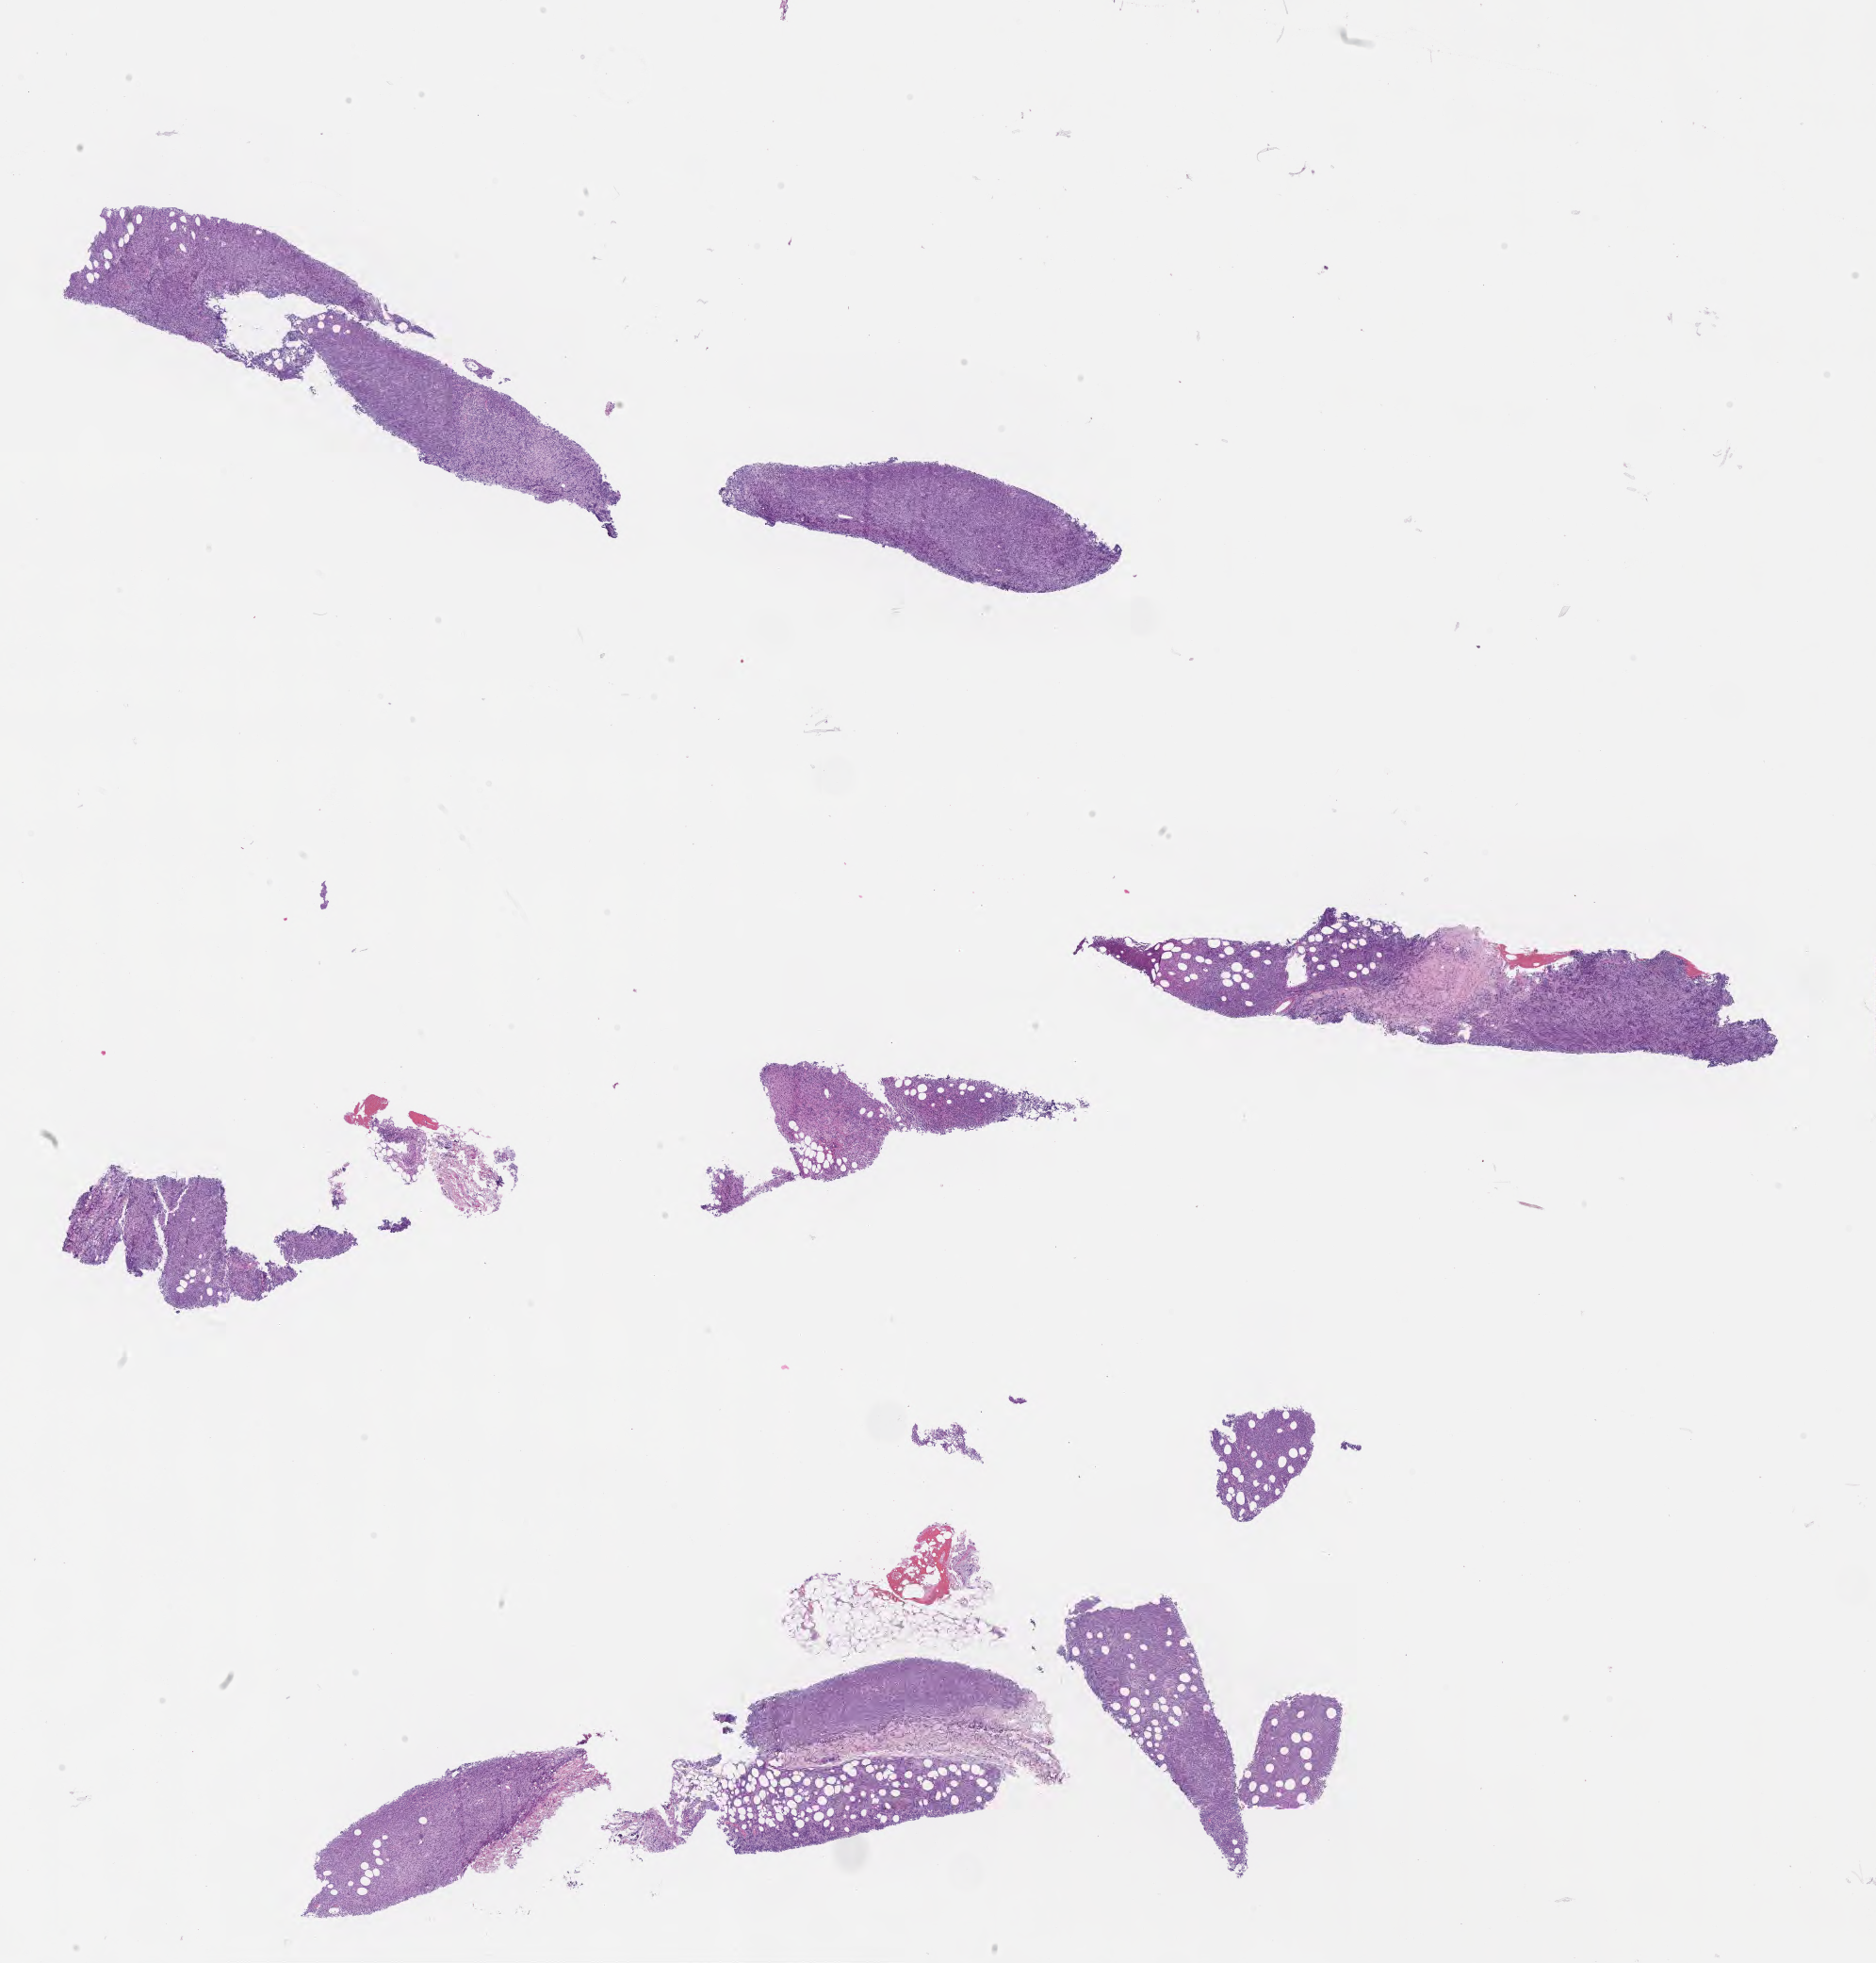
Digitized hematoxylin and eosin (H&E)-stained section — shown as a low-resolution overview of the whole scanned area (about 16.1 x 16.8 mm). Tumor tissue. Patient male; 33 years old.
- histologic diagnosis: Burkitt lymphoma, NOS